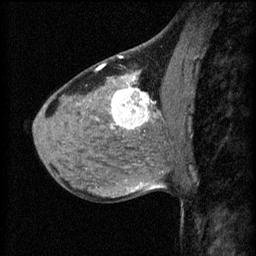
Breast MRI (dynamic contrast-enhanced), one sagittal slice. Position 31 of 60 along the scan axis. 3 images stored at this slice position (order not interpretable as contrast timing). 1.5 T. TE 4.2 ms, TR 8.2 ms. 2.2 mm slice thickness. 256 × 256 image matrix, field of view 180 × 180 mm. Patient: female, 40 years.
Annotated regions visible in this slice (semi-automatically segmented with operator editing):
- analysis volume of interest (the breast-tissue region the enhancement analysis was run in; not a lesion): bounding box <108,82,175,139> (left, top, right, bottom; pixels)
- tumour enhancement mask (voxels above the 70 % enhancement threshold inside the analysis volume of interest): <112,82,159,131>